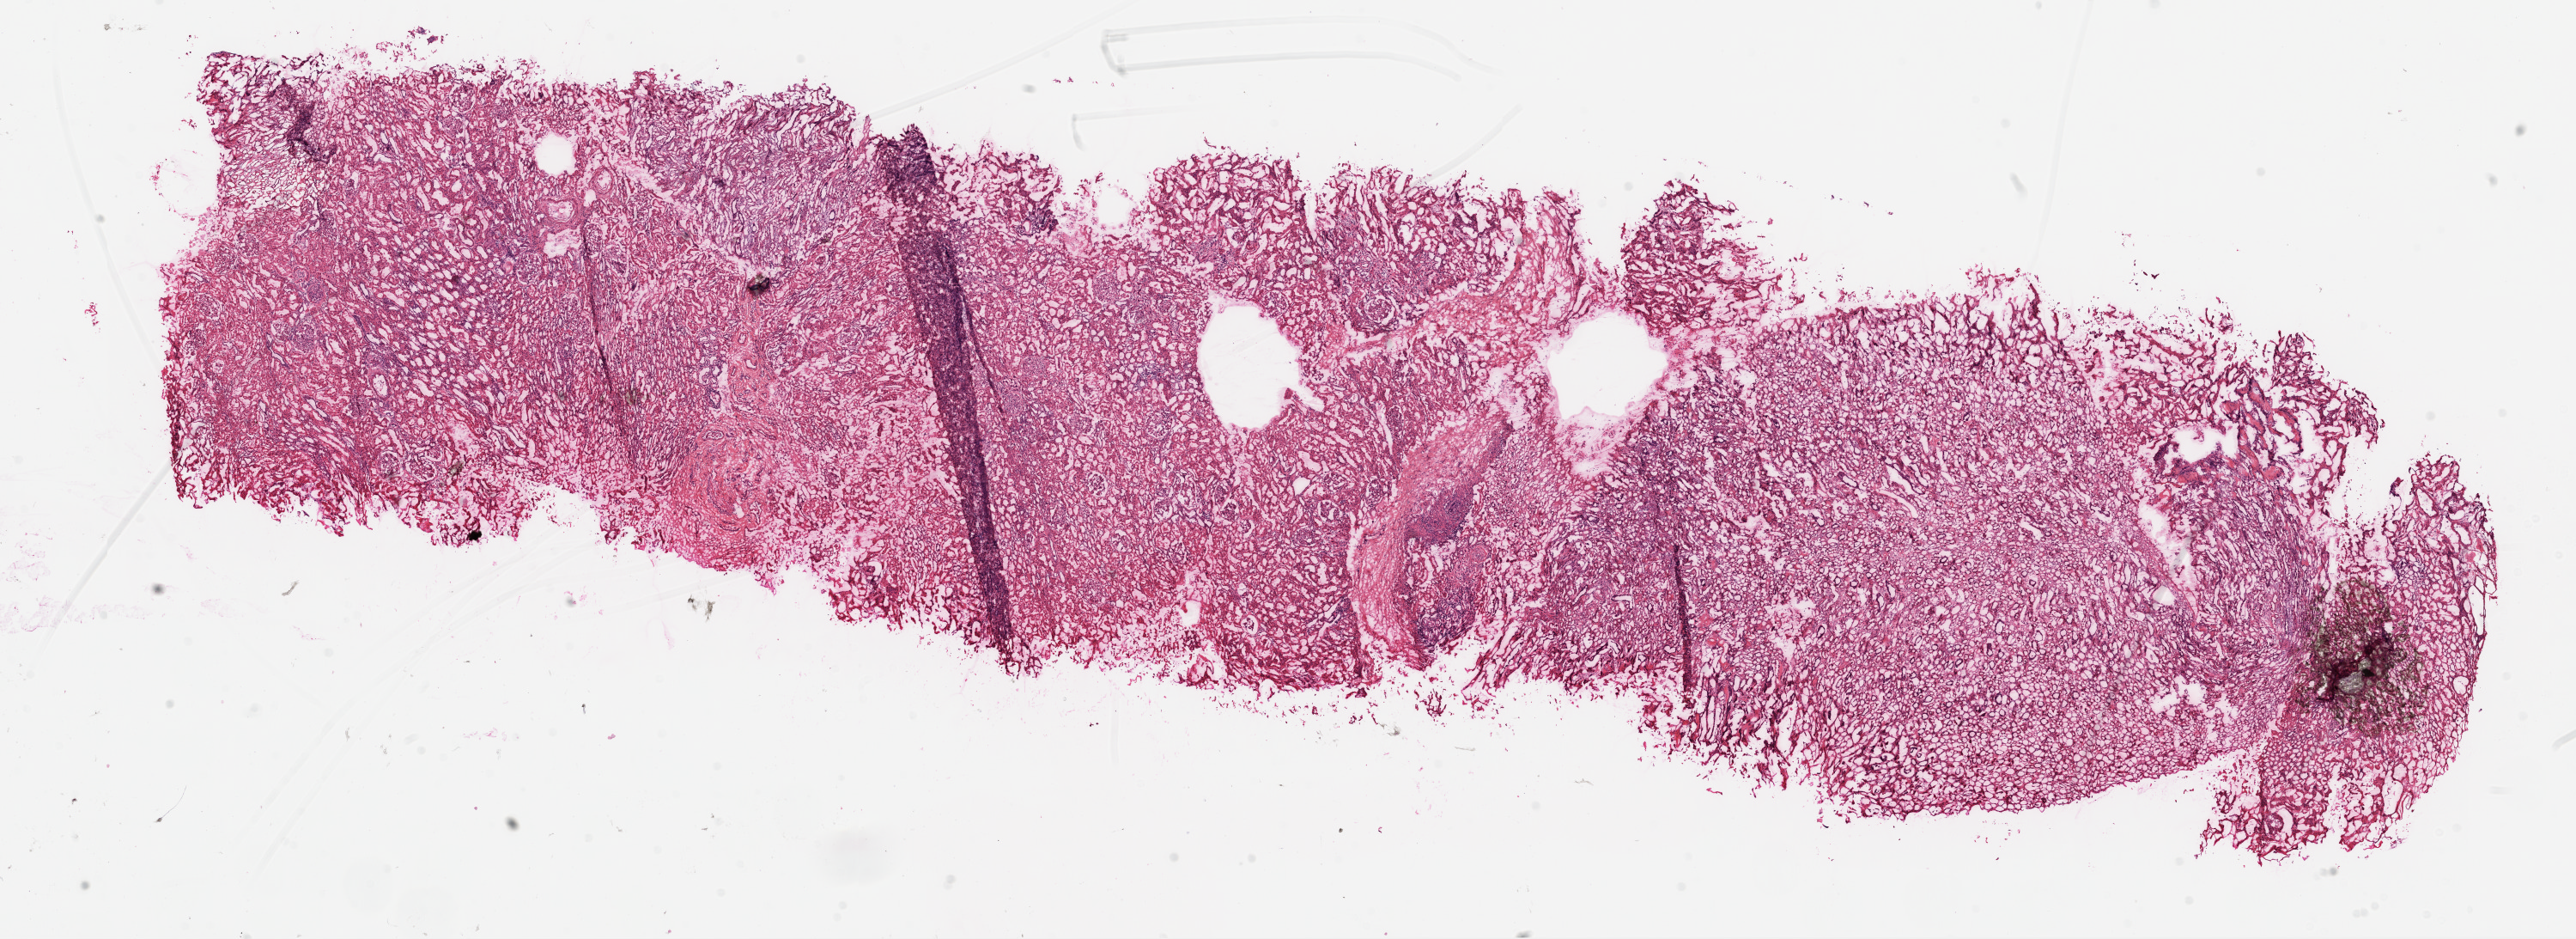
H&E-stained whole-slide image, a low-resolution overview of the entire scanned area, about 24.1 x 8.8 mm, frozen section from the top of the tissue portion, kidney, solid tissue normal (non-tumour tissue) sample. Female patient; age at initial diagnosis 49 years.
This section: solid tissue normal sample (biorepository sample class). Patient diagnosis: Clear cell adenocarcinoma, NOS.